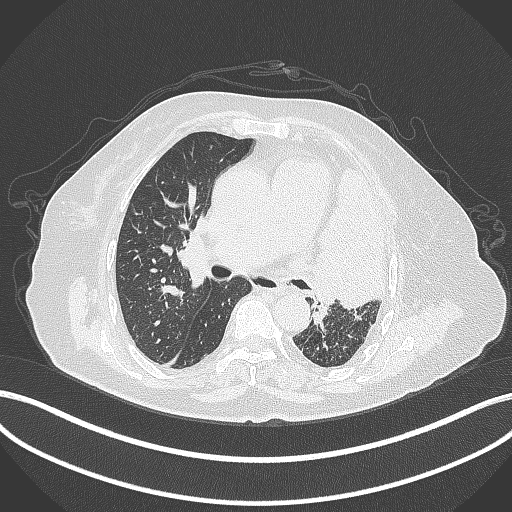
Chest CT, one axial slice. Position 221 of 399 along the scan axis. Reconstruction kernel B70f. 120 kVp. Lung window (W 1500 / L -600 HU). 1 mm slice thickness. 512 × 512 image matrix. Female patient, age 75 years. Case-level facts recorded for this patient, not image findings: clinical TNM (as recorded): T3 N3 M1.
Structures marked on this image (bounding box drawn by a radiologist):
- lung tumour (recorded histology: adenocarcinoma): box from (x=300, y=162) to (x=390, y=316) px